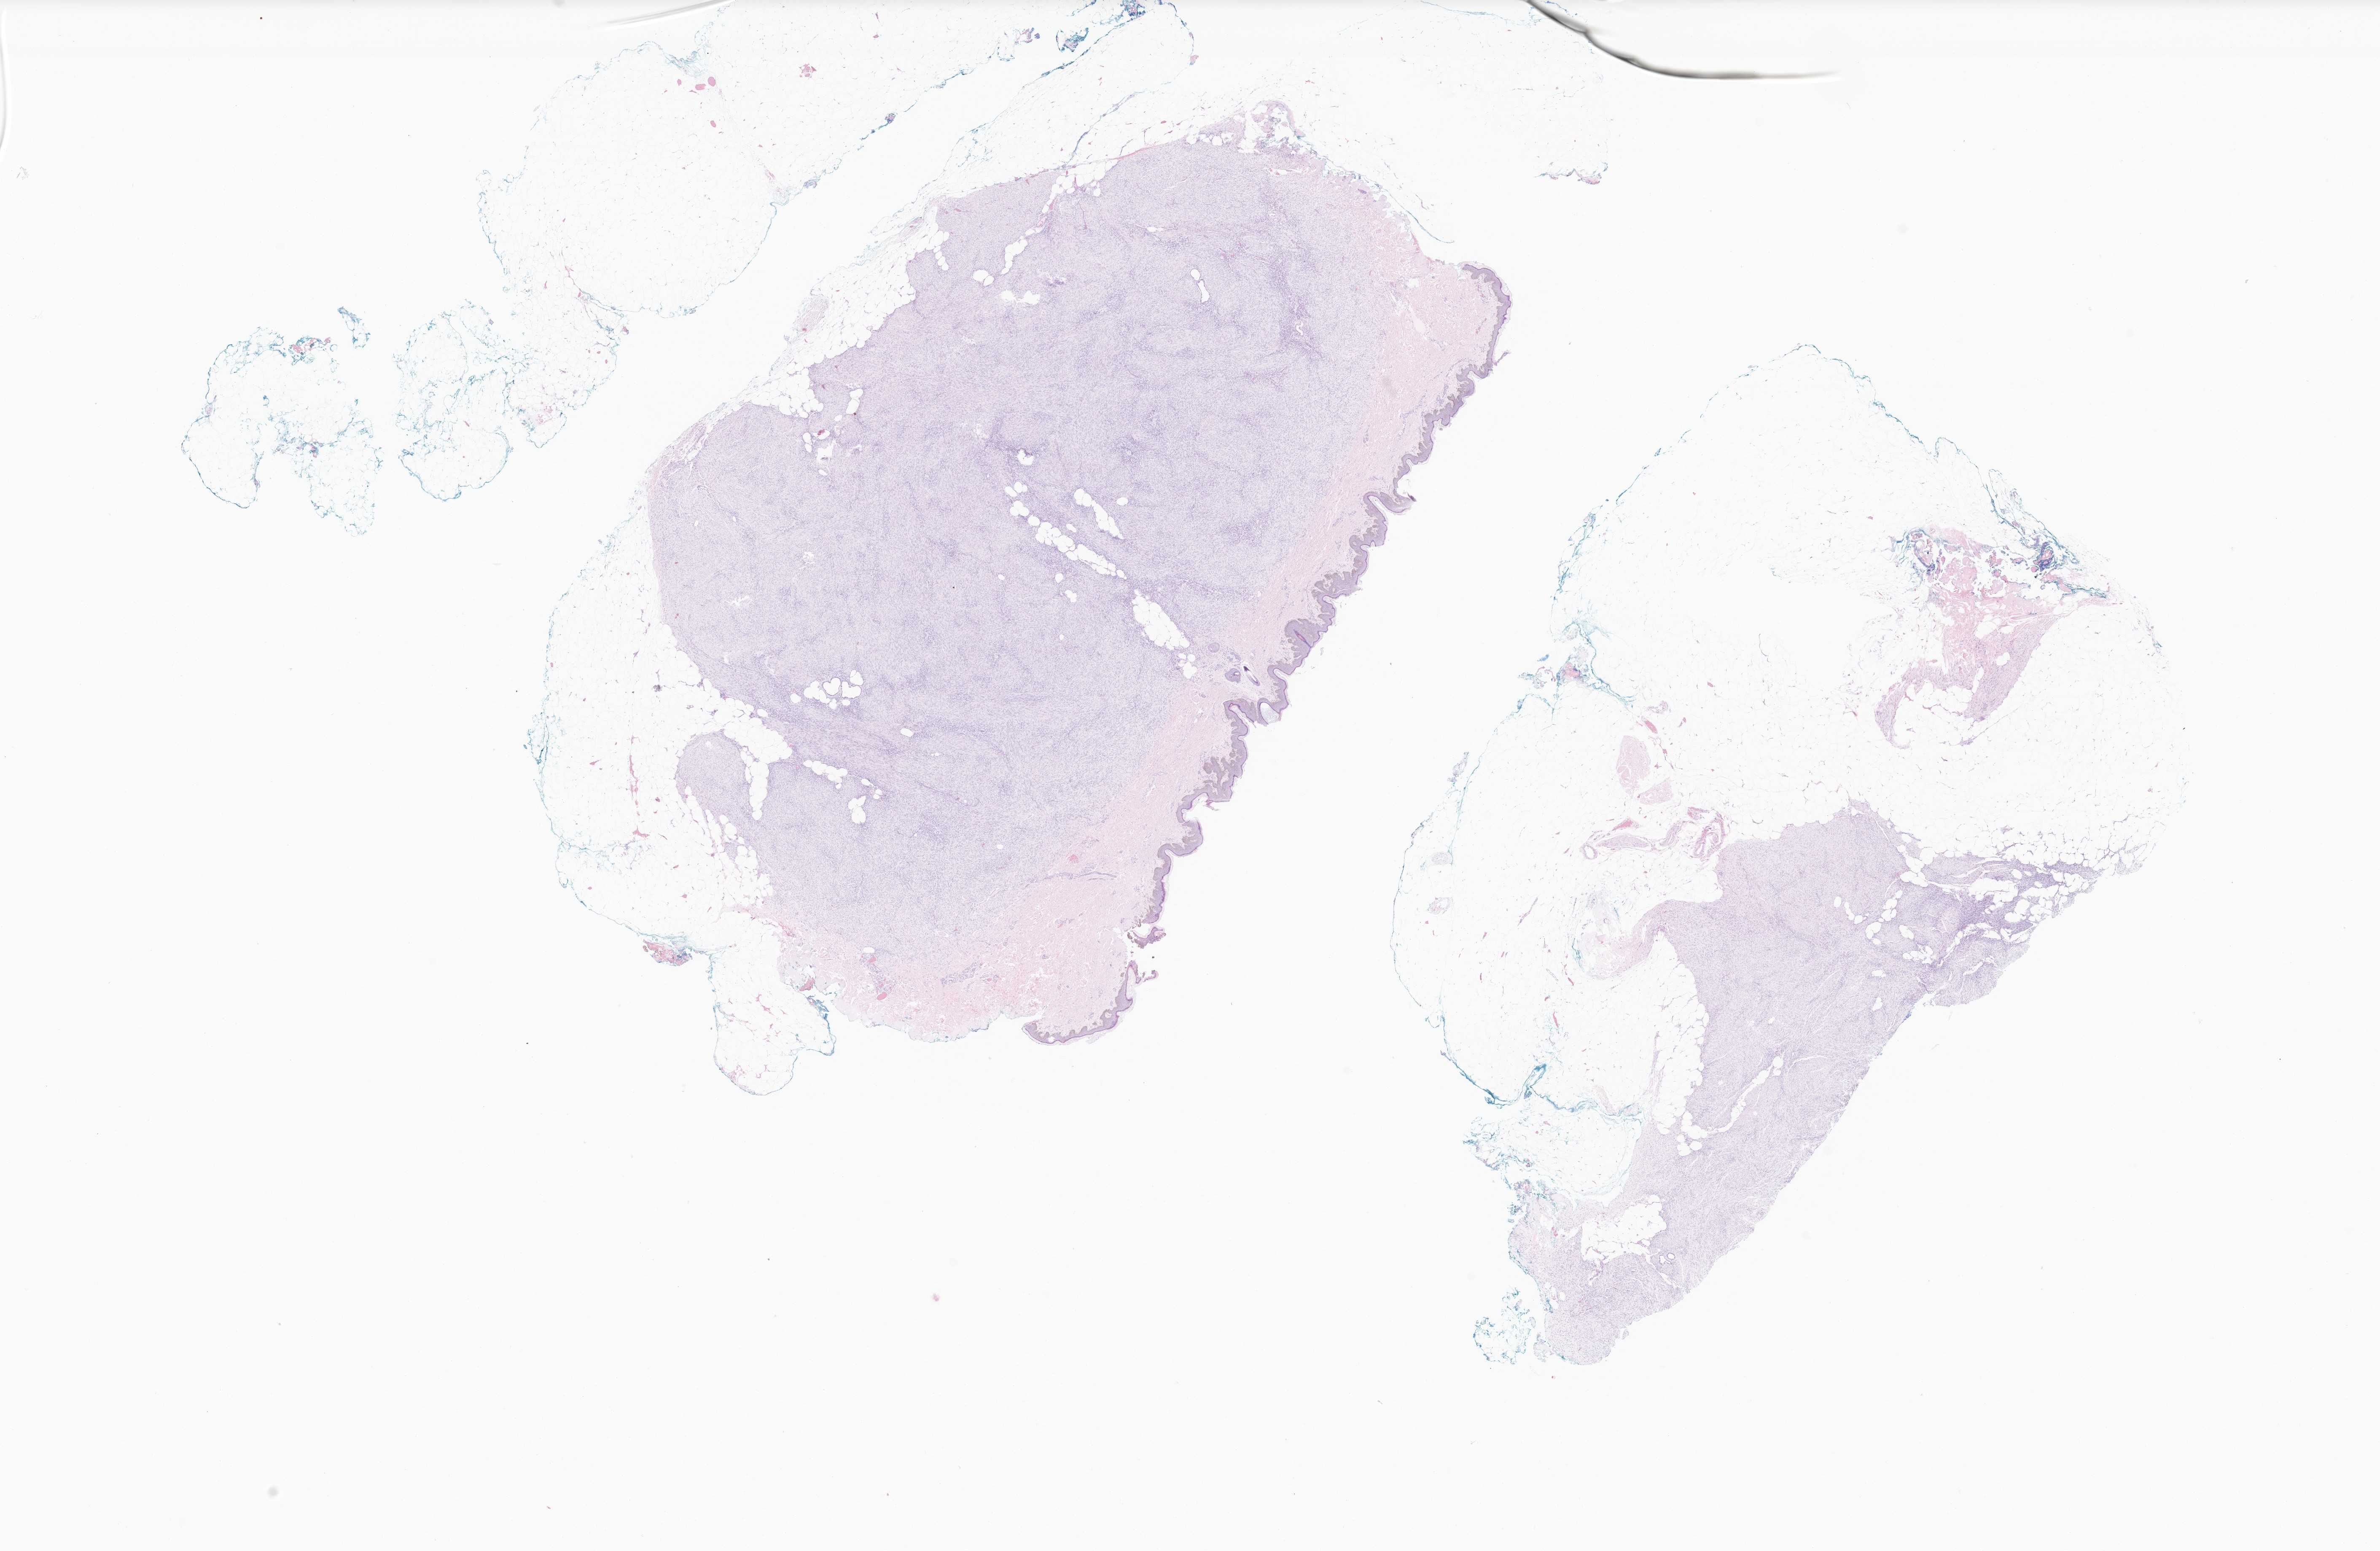
Whole-slide image, hematoxylin and eosin (H&E) stain of tumor tissue from the skin of trunk — shown as a low-resolution overview of the whole scanned area (about 23.8 x 15.5 mm), formalin-fixed paraffin-embedded section. Patient: female, age 106 months (8 years 10 months).
Diagnosis (ICD-O-3 morphology term): Dermatofibrosarcoma protuberans, fibrosarcomatous.